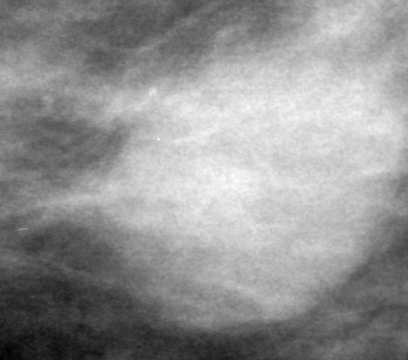
Region of interest cut from a scanned film mammogram (one marked finding); right breast; MLO view; BI-RADS breast density category 3 (scale 1–4).
Finding: mass, shape oval, margins obscured; BI-RADS assessment category 0 (incomplete: needs additional imaging); pathology (as recorded): benign.